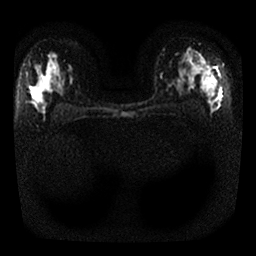
Breast MRI, one axial slice; position 19 of 25 along the scan axis; diffusion-weighted series; image 2 of 4 stored at this slice position (different b-values; order by instance number); 1.5 T; 256 × 256 image matrix, field of view 320 × 320 mm. Female patient.
Structures marked on this image (manually delineated by an expert):
- tumour on diffusion-weighted imaging: bounding box <200,59,214,77> (left, top, right, bottom; pixels)